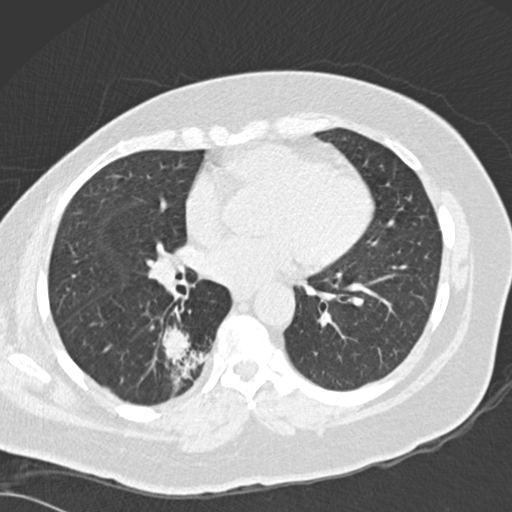
Low-dose screening chest CT, axial slice; baseline annual screen; lung window (W 1500 / L -600 HU); slice 90 of 162 in the series; 512 × 512 image matrix. Female participant, aged 66 years at enrolment. Current smoker at enrolment.
Expert reader's lesion annotation, box from (x=153, y=324) to (x=224, y=396) px. The screening reader recorded 3 non-calcified nodules or masses ≥4 mm on this exam (left lower lobe, left lower lobe, right lower lobe); which of them this box marks is not recorded.